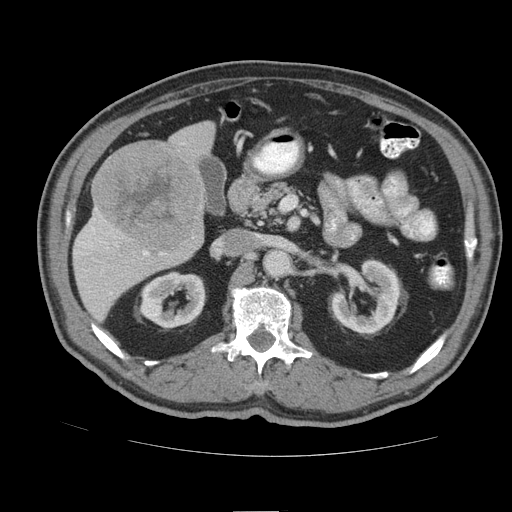
Contrast-enhanced abdominal CT (liver protocol), one axial slice; position 41 of 105 along the scan axis; reconstruction kernel STANDARD; 140 kVp; soft-tissue window (W 400 / L 40 HU); 2.5 mm slice thickness; 512 × 512 image matrix. Case-level facts recorded for this patient, not image findings: diagnosis: hepatocellular carcinoma (patient treated with transarterial chemoembolisation; whether this scan precedes or follows treatment is not stated here); TNM stage (as recorded): Stage-IIIB; Child-Pugh class: A; tumour nodularity: multinodular.
Annotated regions visible in this slice (semi-automatically segmented with operator editing):
- liver parenchyma outside the tumour (the mass and vessels are separate outlines, so this box may not span the whole liver): box from (x=72, y=121) to (x=214, y=320) px
- mass: (x=93, y=142)–(x=204, y=251)
- liver vessels: (x=78, y=143)–(x=184, y=294)